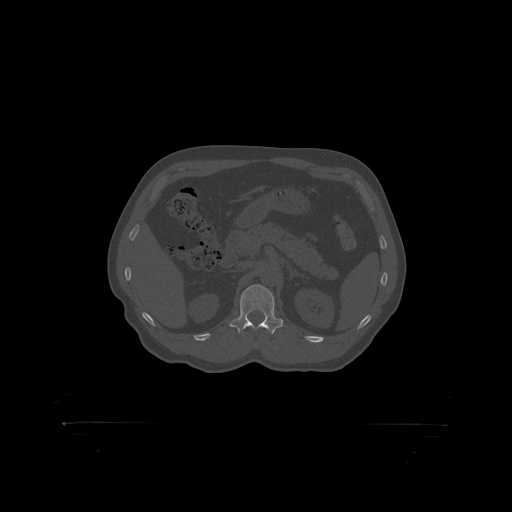
CT including the spine, one axial slice. Slice 329 of 399 in the series (ordered by position). 120 kVp. Bone window (W 1800 / L 400 HU). 1.25 mm slice thickness. 512 × 512 image matrix, field of view 650 × 650 mm. Male patient, age 46 years. From the clinical record (not read from this slice): primary cancer: skin.
Annotated regions visible in this slice (semi-automatic segmentation, software-assisted and operator-edited):
- L1 vertebra: bounding box (x1, y1, x2, y2) in pixels: (240, 285, 275, 319)